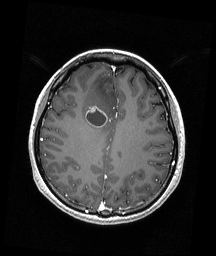
Brain MRI from a brain-tumour surgery series, one axial slice; position 66 of 192 along the scan axis; T1-weighted post-contrast; 1 mm slice thickness; 216 × 256 image matrix, field of view 211 × 250 mm. From the clinical record (not read from this slice): histopathology: Astrocytoma; WHO grade: 4; IDH mutation: yes.
Outlined on this slice (outlined manually by an expert reader):
- tumour: bounding box (x1, y1, x2, y2) in pixels: (85, 106, 108, 127)